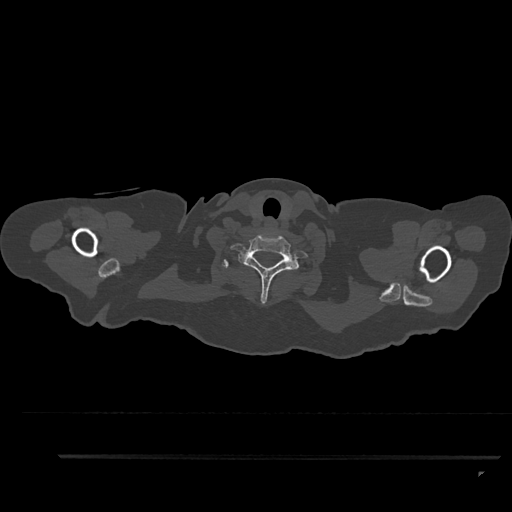
CT including the spine, one axial slice; slice 791 of 797 in the series (ordered by position); reconstruction kernel Br40s/3; bone window (W 1800 / L 400 HU); 0.5 mm slice thickness; 512 × 512 image matrix. Female patient, age 44 years. Case-level facts recorded for this patient, not image findings: primary cancer: renal.
Outlined on this slice (semi-automatic segmentation, software-assisted and operator-edited):
- T1 vertebra: bounding box (x1, y1, x2, y2) in pixels: (222, 259, 299, 268)